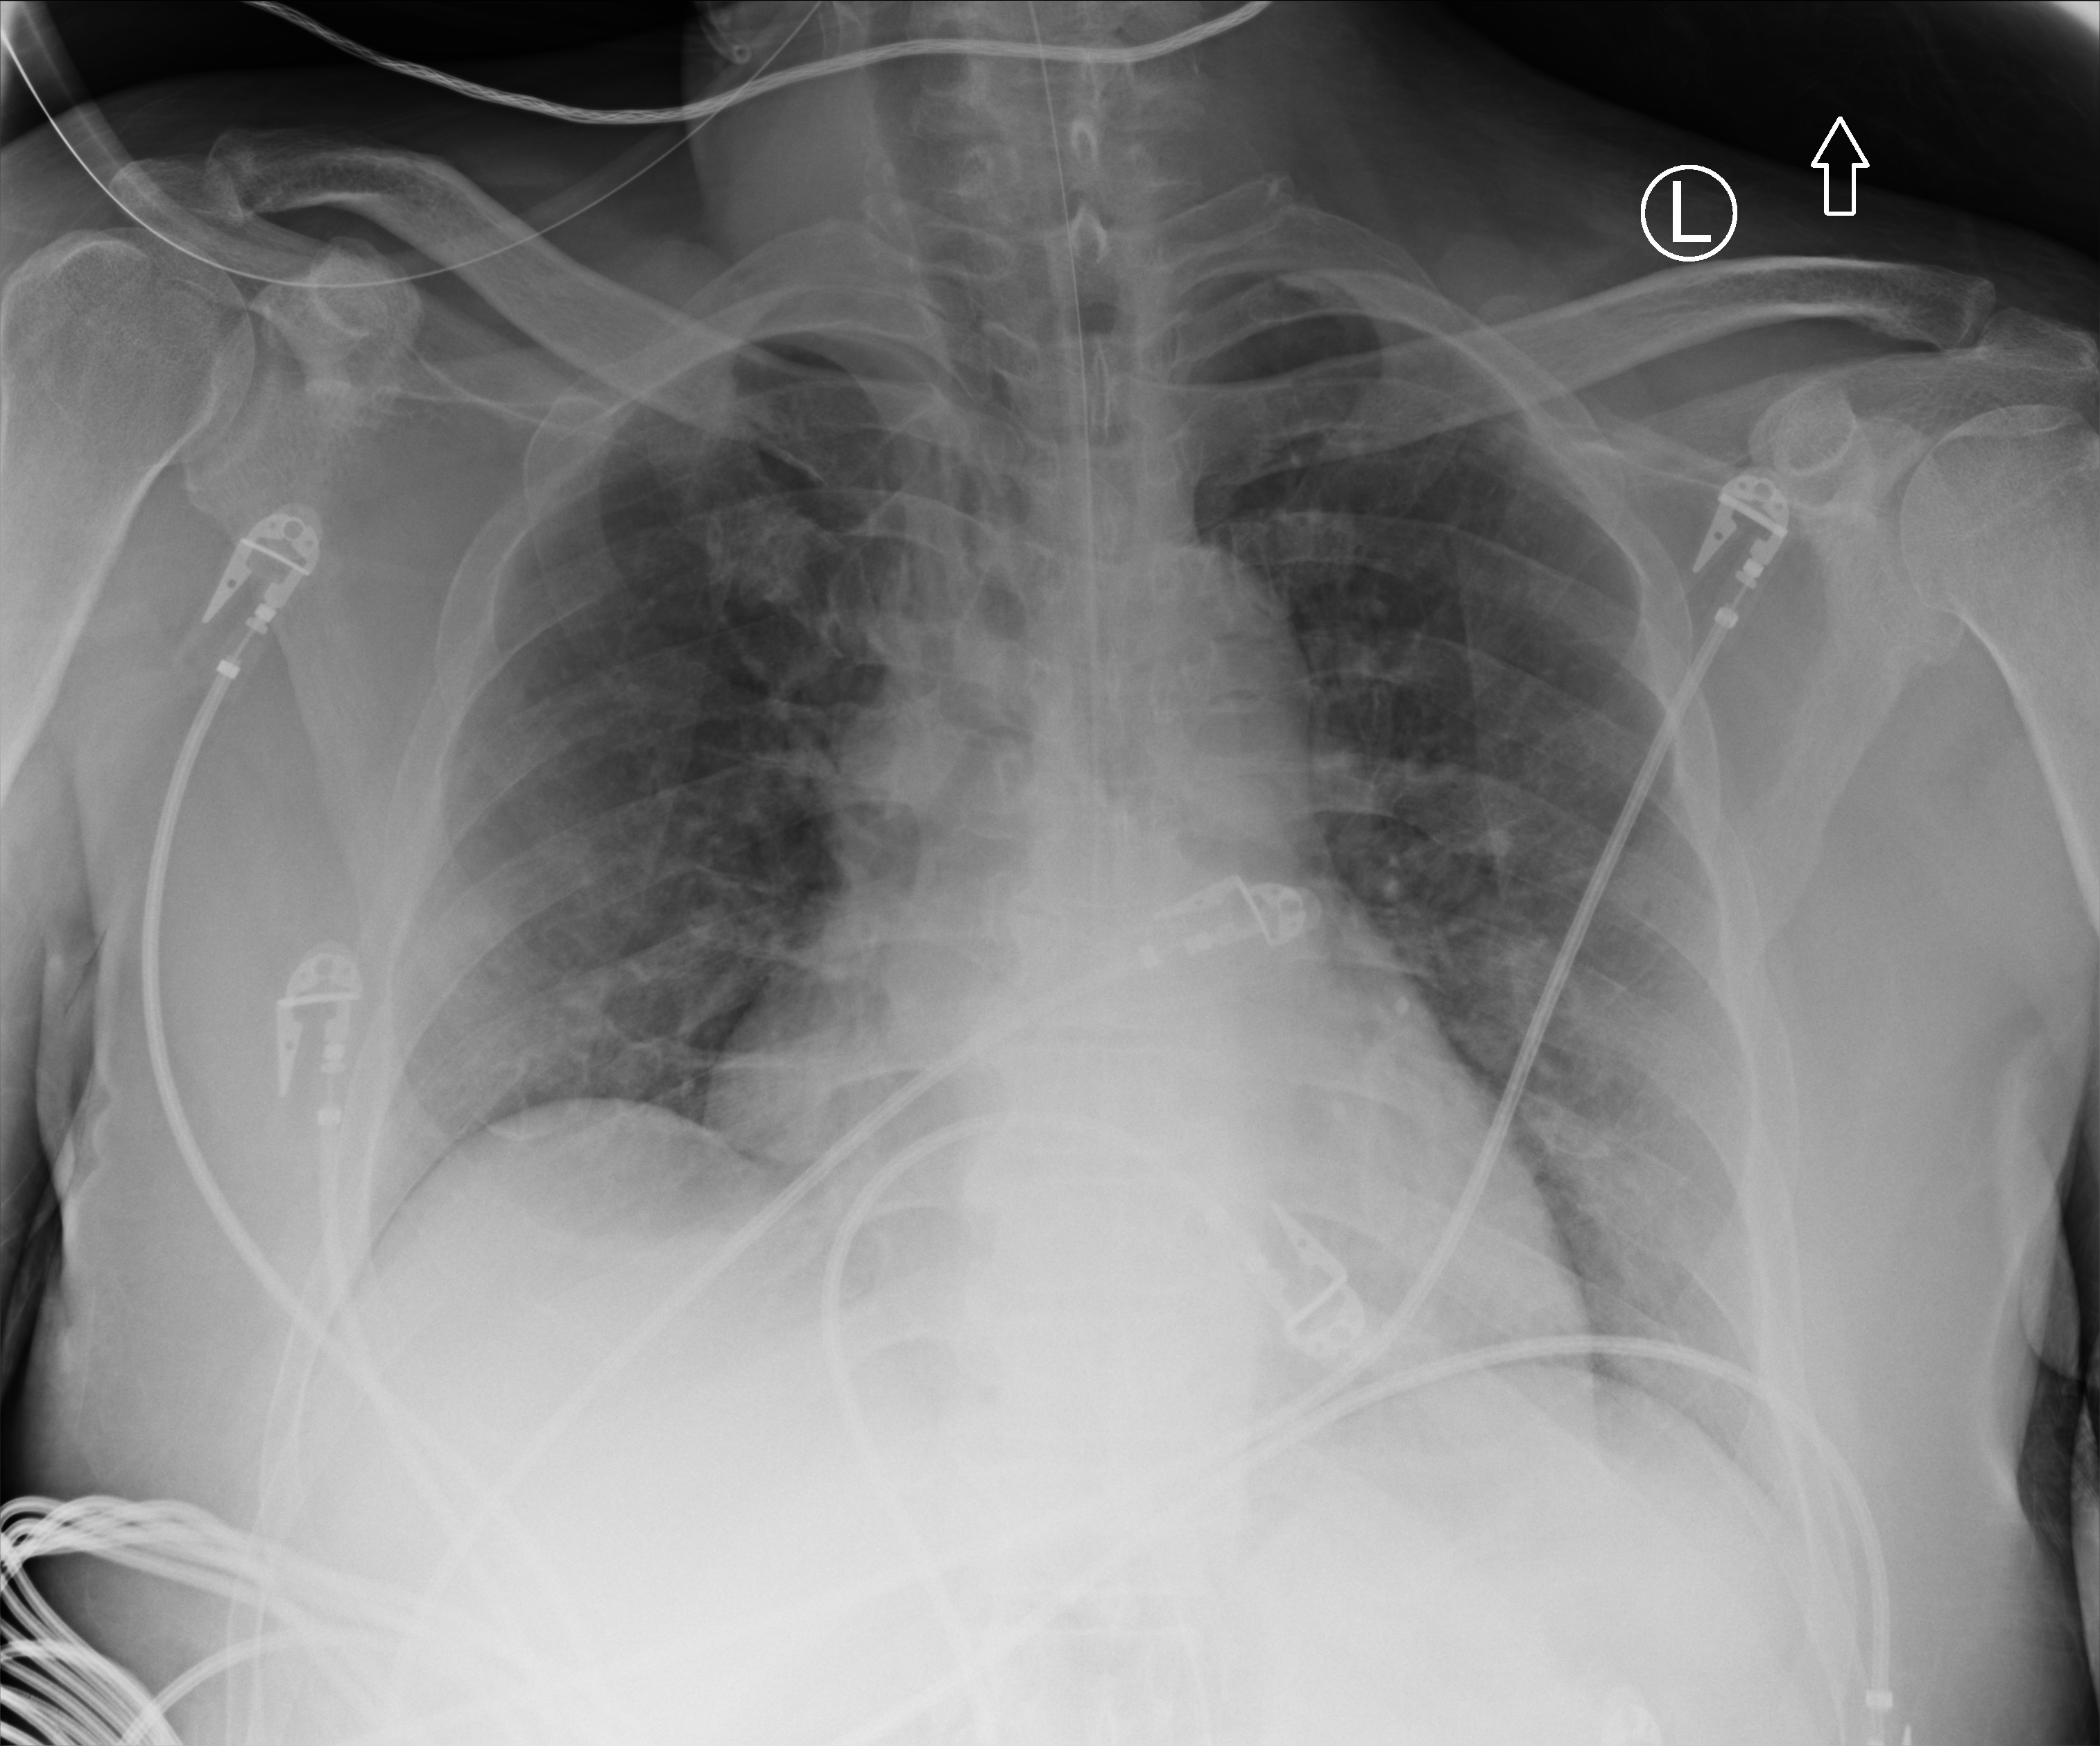
Chest X-ray (portable); anteroposterior (AP) projection. Patient hospitalised with COVID-19, aged 18–59 years.
From the hospital-stay record, not from the radiograph (when in the stay this image was taken is not recorded):
- admitted to intensive care during this hospital stay: yes